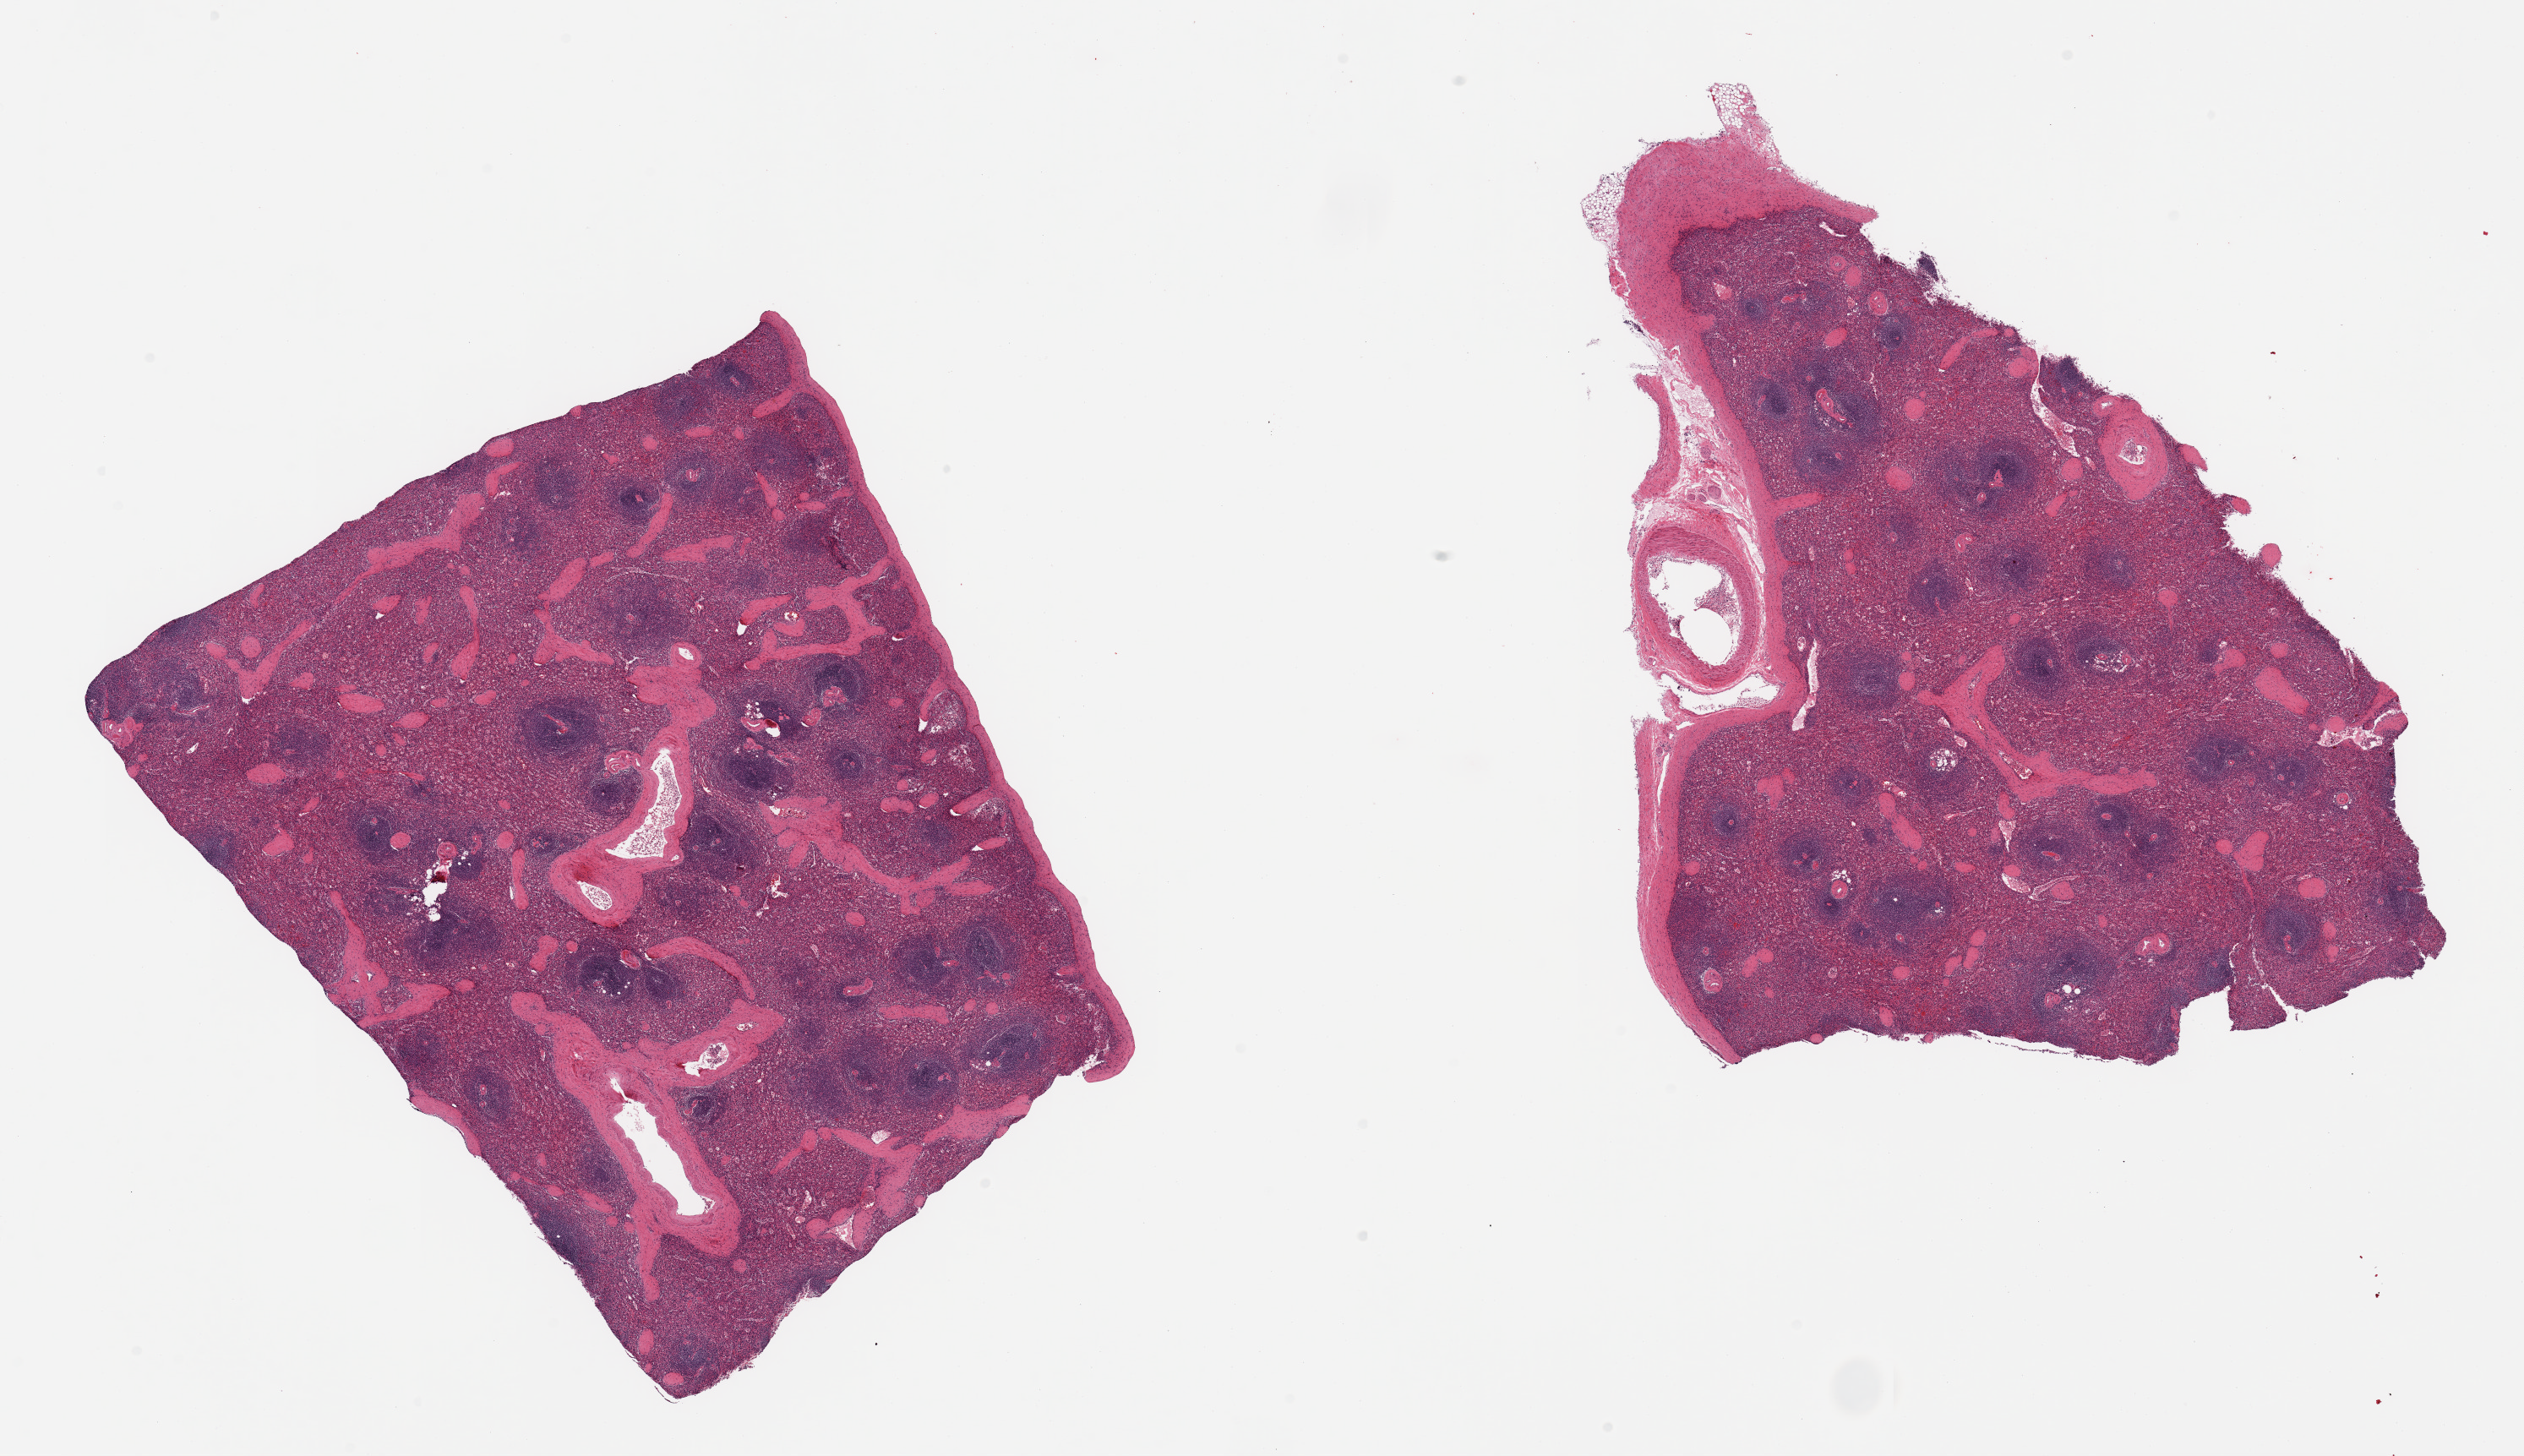
Digitized hematoxylin and eosin (H&E)-stained section — a low-resolution overview of the entire scanned area, about 23.6 x 13.6 mm. PAXgene-fixed paraffin-embedded (PFPE) section. Section of spleen (target tissue). Tissue donor sample.
Pathologist's review note for this sample: 2 pieces, no abnormalities.